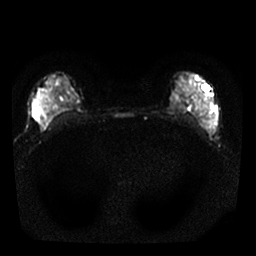
Breast MRI, one axial slice. Slice 15 of 25 in the series (ordered by position). Diffusion-weighted series; image 2 of 4 stored at this slice position (different b-values; order by instance number). 1.5 T. 4 mm slice thickness. 256 × 256 image matrix. Female patient.
Annotated regions visible in this slice (manually delineated by an expert):
- tumour on diffusion-weighted imaging: box from (x=33, y=115) to (x=48, y=128) px